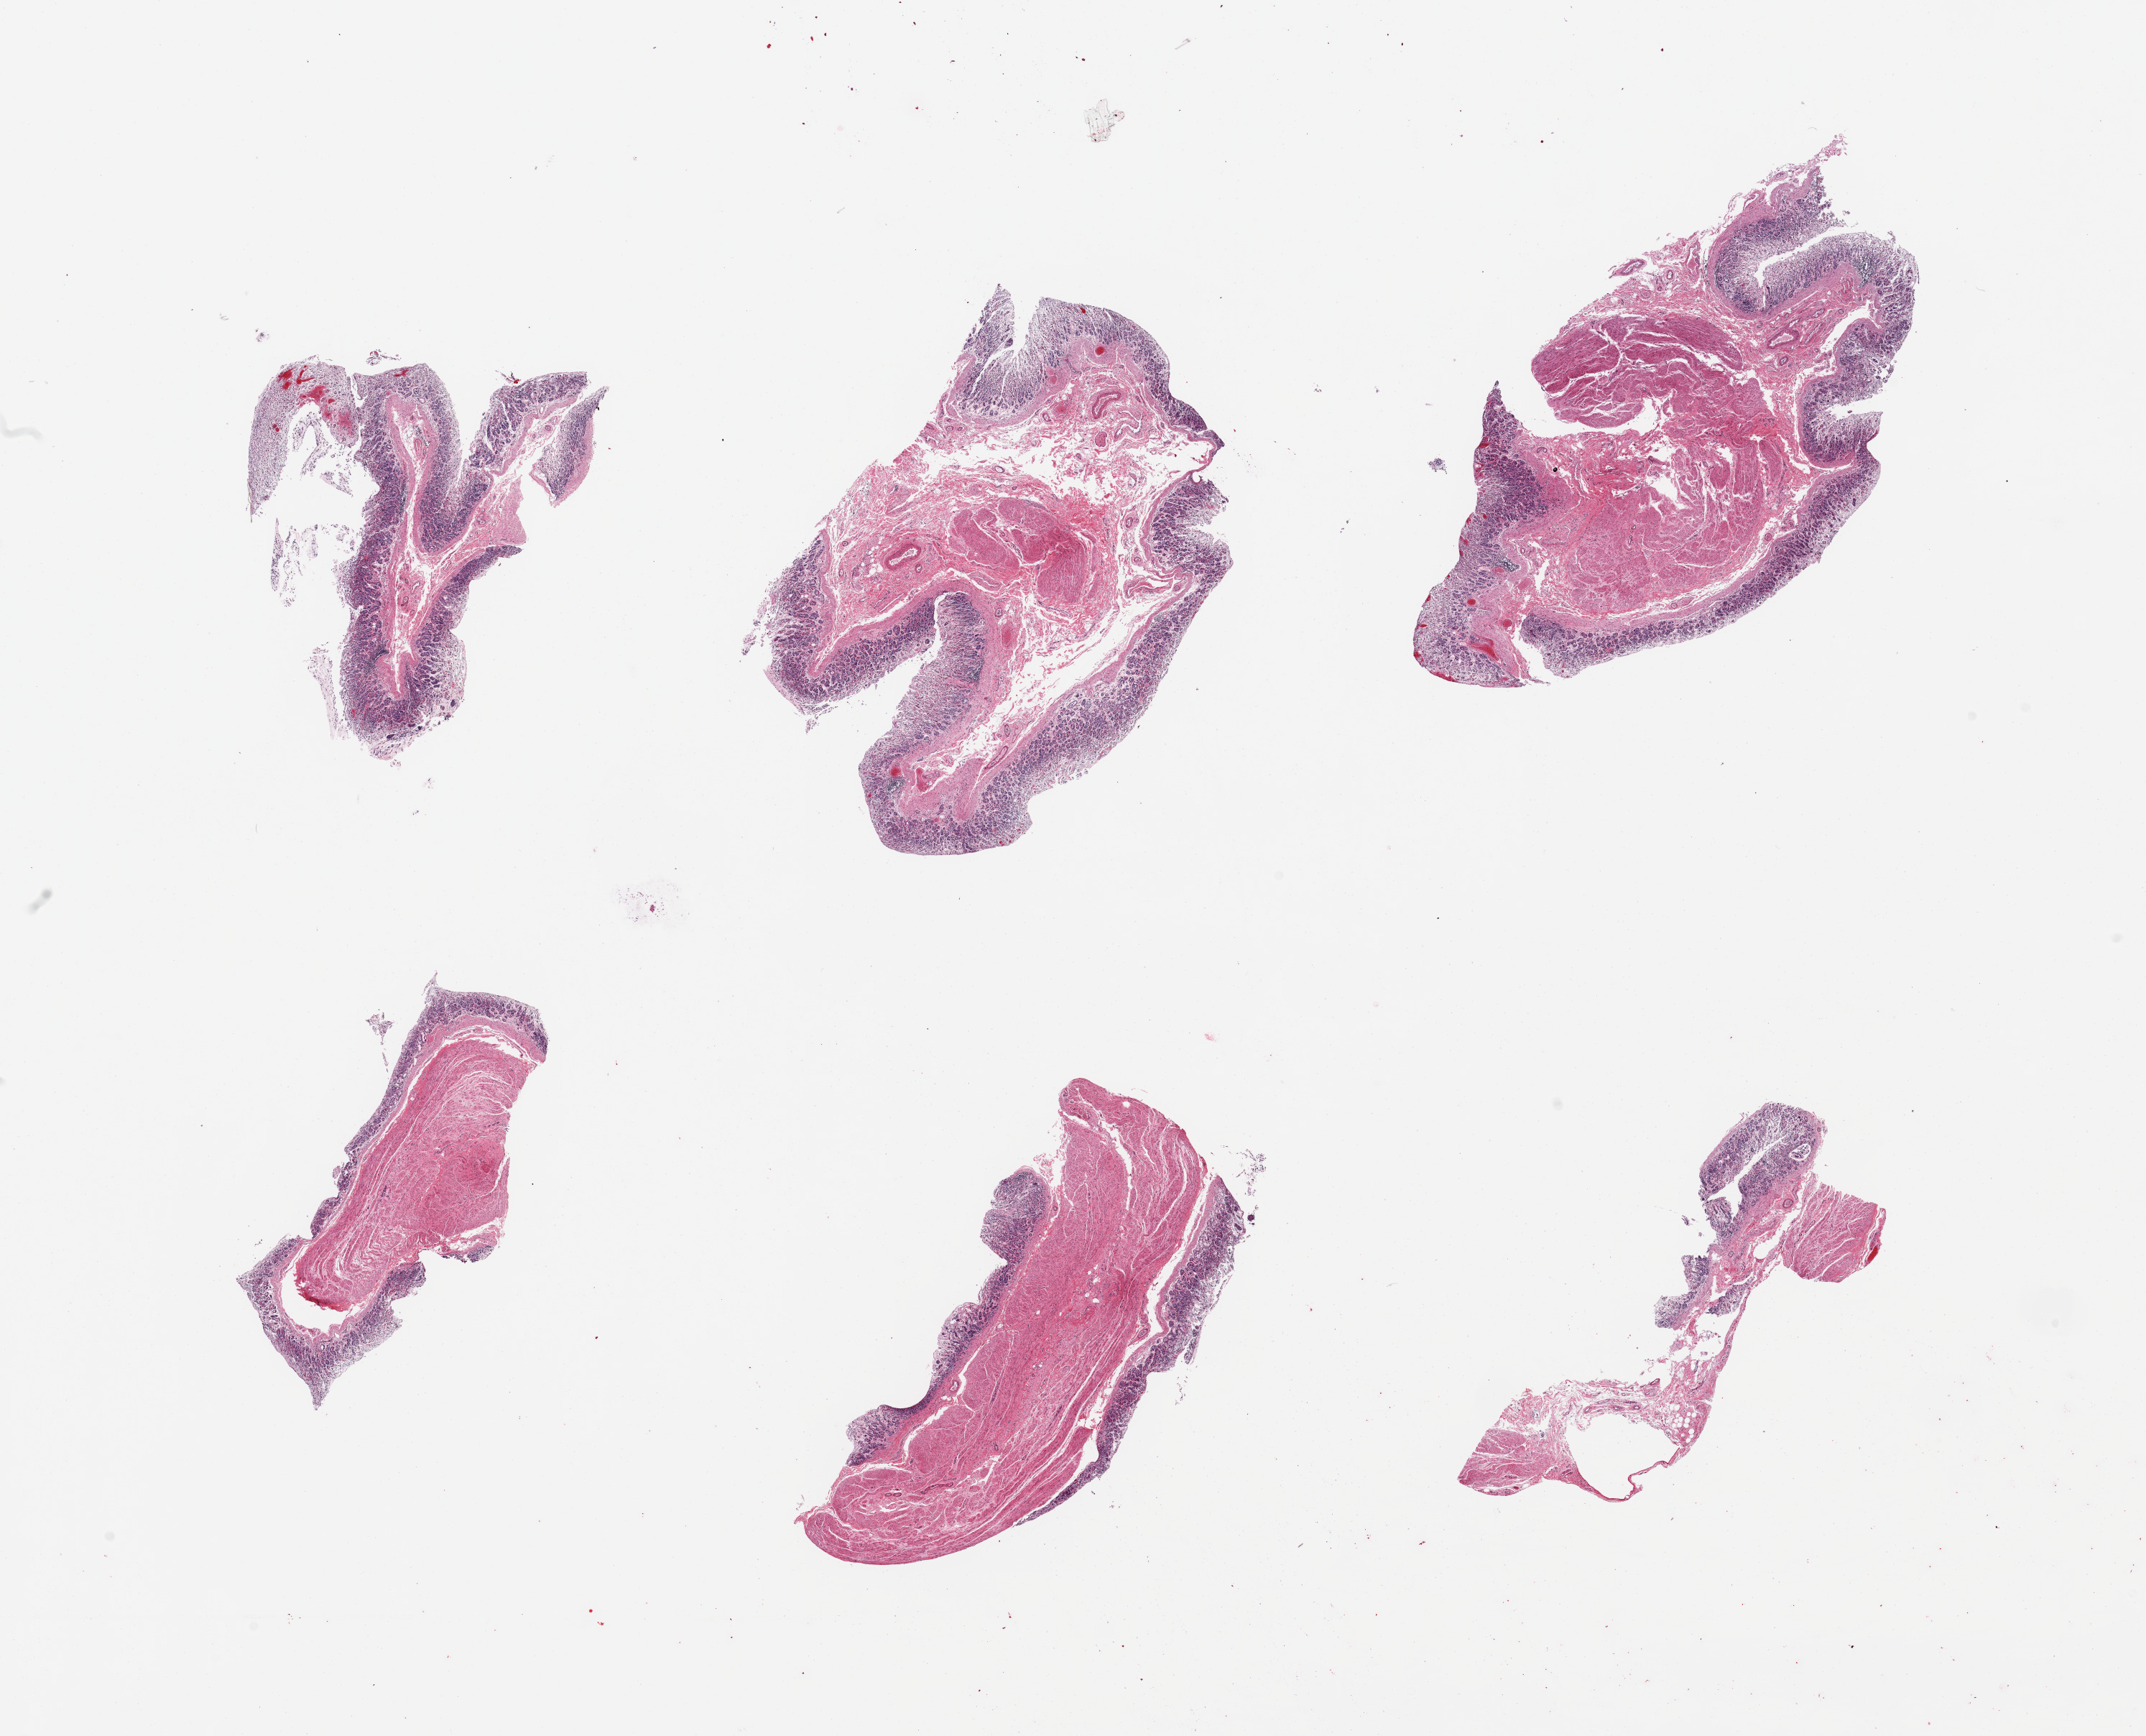
H&E whole-slide image, whole scanned area (about 23.6 x 19.1 mm, acquisition: 20x scan) shown as a low-resolution overview; PAXgene-fixed paraffin-embedded (PFPE) section; sampled site (target tissue): stomach; tissue donor sample. Donor: female.
* review note (as recorded): 6 pieces, mucosa up to ~0.6mm but with moderate to advanced auutolysis